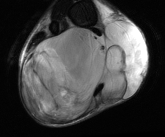
MRI of an extremity soft-tissue mass, one axial slice. Position 28 of 81 along the scan axis. T2-weighted fat-saturated. MR volume resampled by the dataset authors to the PET/CT grid (not the native acquisition matrix). 165 × 137 image matrix, field of view 161 × 134 mm. Male patient. From the clinical record (not read from this slice): histological type: liposarcoma - round cell; grade: high; site of the primary tumour: right calf.
Outlined on this slice (expert contour drawn on MRI and transferred to this co-registered scan by the dataset authors):
- gross tumour volume (mass): bounding box [x1, y1, x2, y2] px = [21, 18, 149, 120]